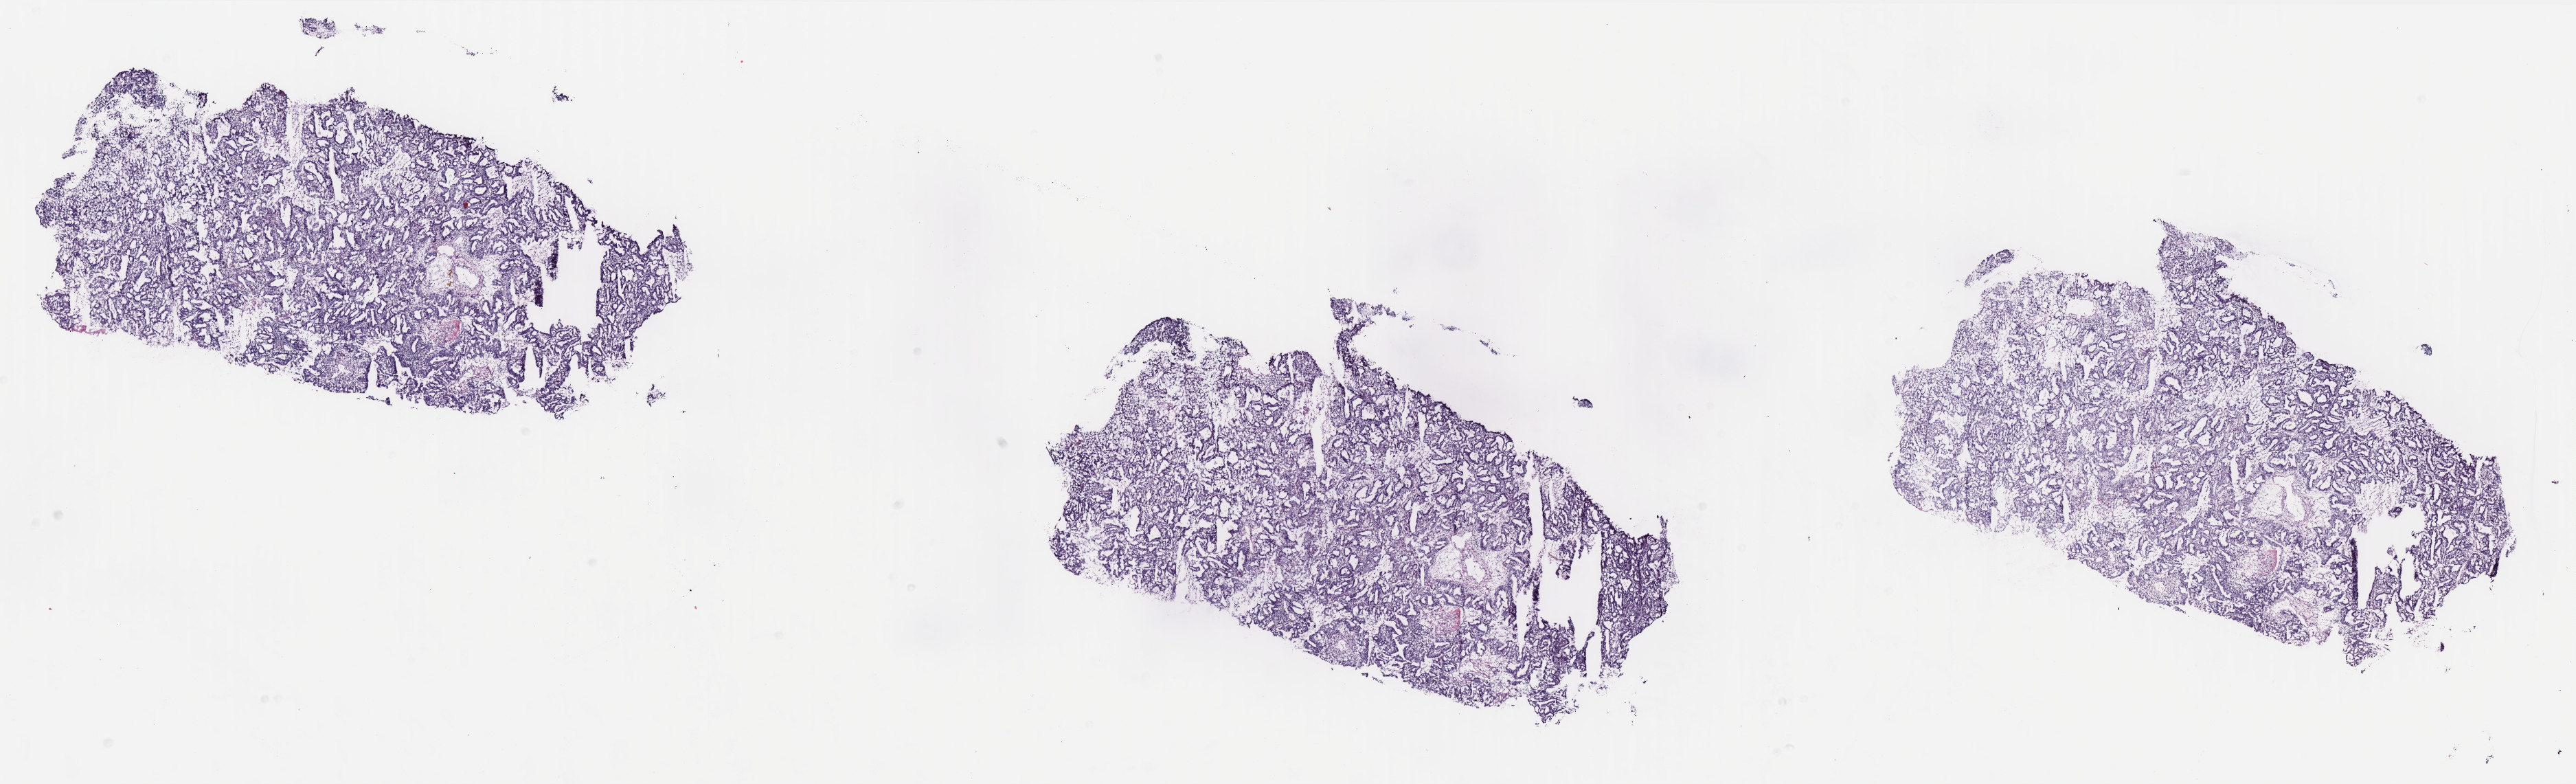
H&E-stained whole-slide image, shown as a low-resolution overview of the whole scanned area (about 30.1 x 9.1 mm, slide scanned at 40x), frozen section from the top of the tissue portion, primary tumour sample from the uterus. Female, age 65 years at initial diagnosis. Histologic grade: G1 (well differentiated). Composition of this section per pathologist review: tumour cells 100%, tumour nuclei 80%, normal cells 0%, stromal cells 0%, necrosis 0%. Infiltration values recorded for this section: lymphocyte infiltration 1%, monocyte infiltration 0%, neutrophil infiltration 0%.
Histologic diagnosis: Endometrioid adenocarcinoma, NOS (endometrium). FIGO stage: IB.